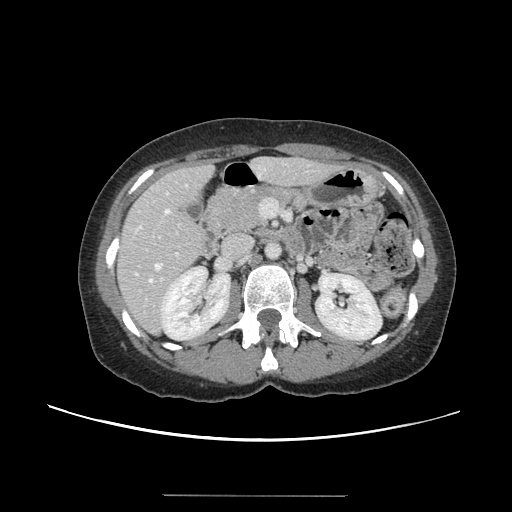
Contrast-enhanced abdominal CT, one axial slice. Position 65 of 144 along the scan axis. Intravenous contrast given. Soft-tissue window (W 400 / L 40 HU). 512 × 512 image matrix, field of view 380 × 380 mm. Female patient, age 53 years. Case-level facts recorded for this patient, not image findings: diagnosis: colorectal cancer liver metastases, imaged before liver resection; multiple liver metastases: yes; largest metastasis: 1.1 cm.
Structures marked on this image (outlined manually by an expert reader):
- hepatic veins: box from (x=136, y=185) to (x=187, y=282) px
- liver: (x=119, y=159)–(x=335, y=333)
- planned liver remnant (the part of the liver to remain after resection): (x=119, y=158)–(x=326, y=307)
- portal vein (with intrahepatic branches): (x=160, y=253)–(x=179, y=281)